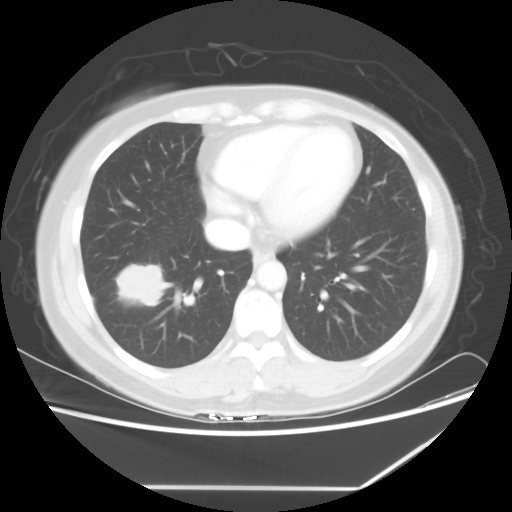
Chest CT, one axial slice; slice 22 of 60 in the series (ordered by position); reconstruction kernel STANDARD; lung window (W 1500 / L -600 HU); 512 × 512 image matrix, field of view 374 × 374 mm. Patient: female, 42 years. From the clinical record (not read from this slice): clinical TNM (as recorded): T2 N1 M0.
Annotated regions visible in this slice (rectangle marked by the reading radiologist):
- lung tumour (recorded histology: adenocarcinoma): box from (x=112, y=261) to (x=172, y=308) px